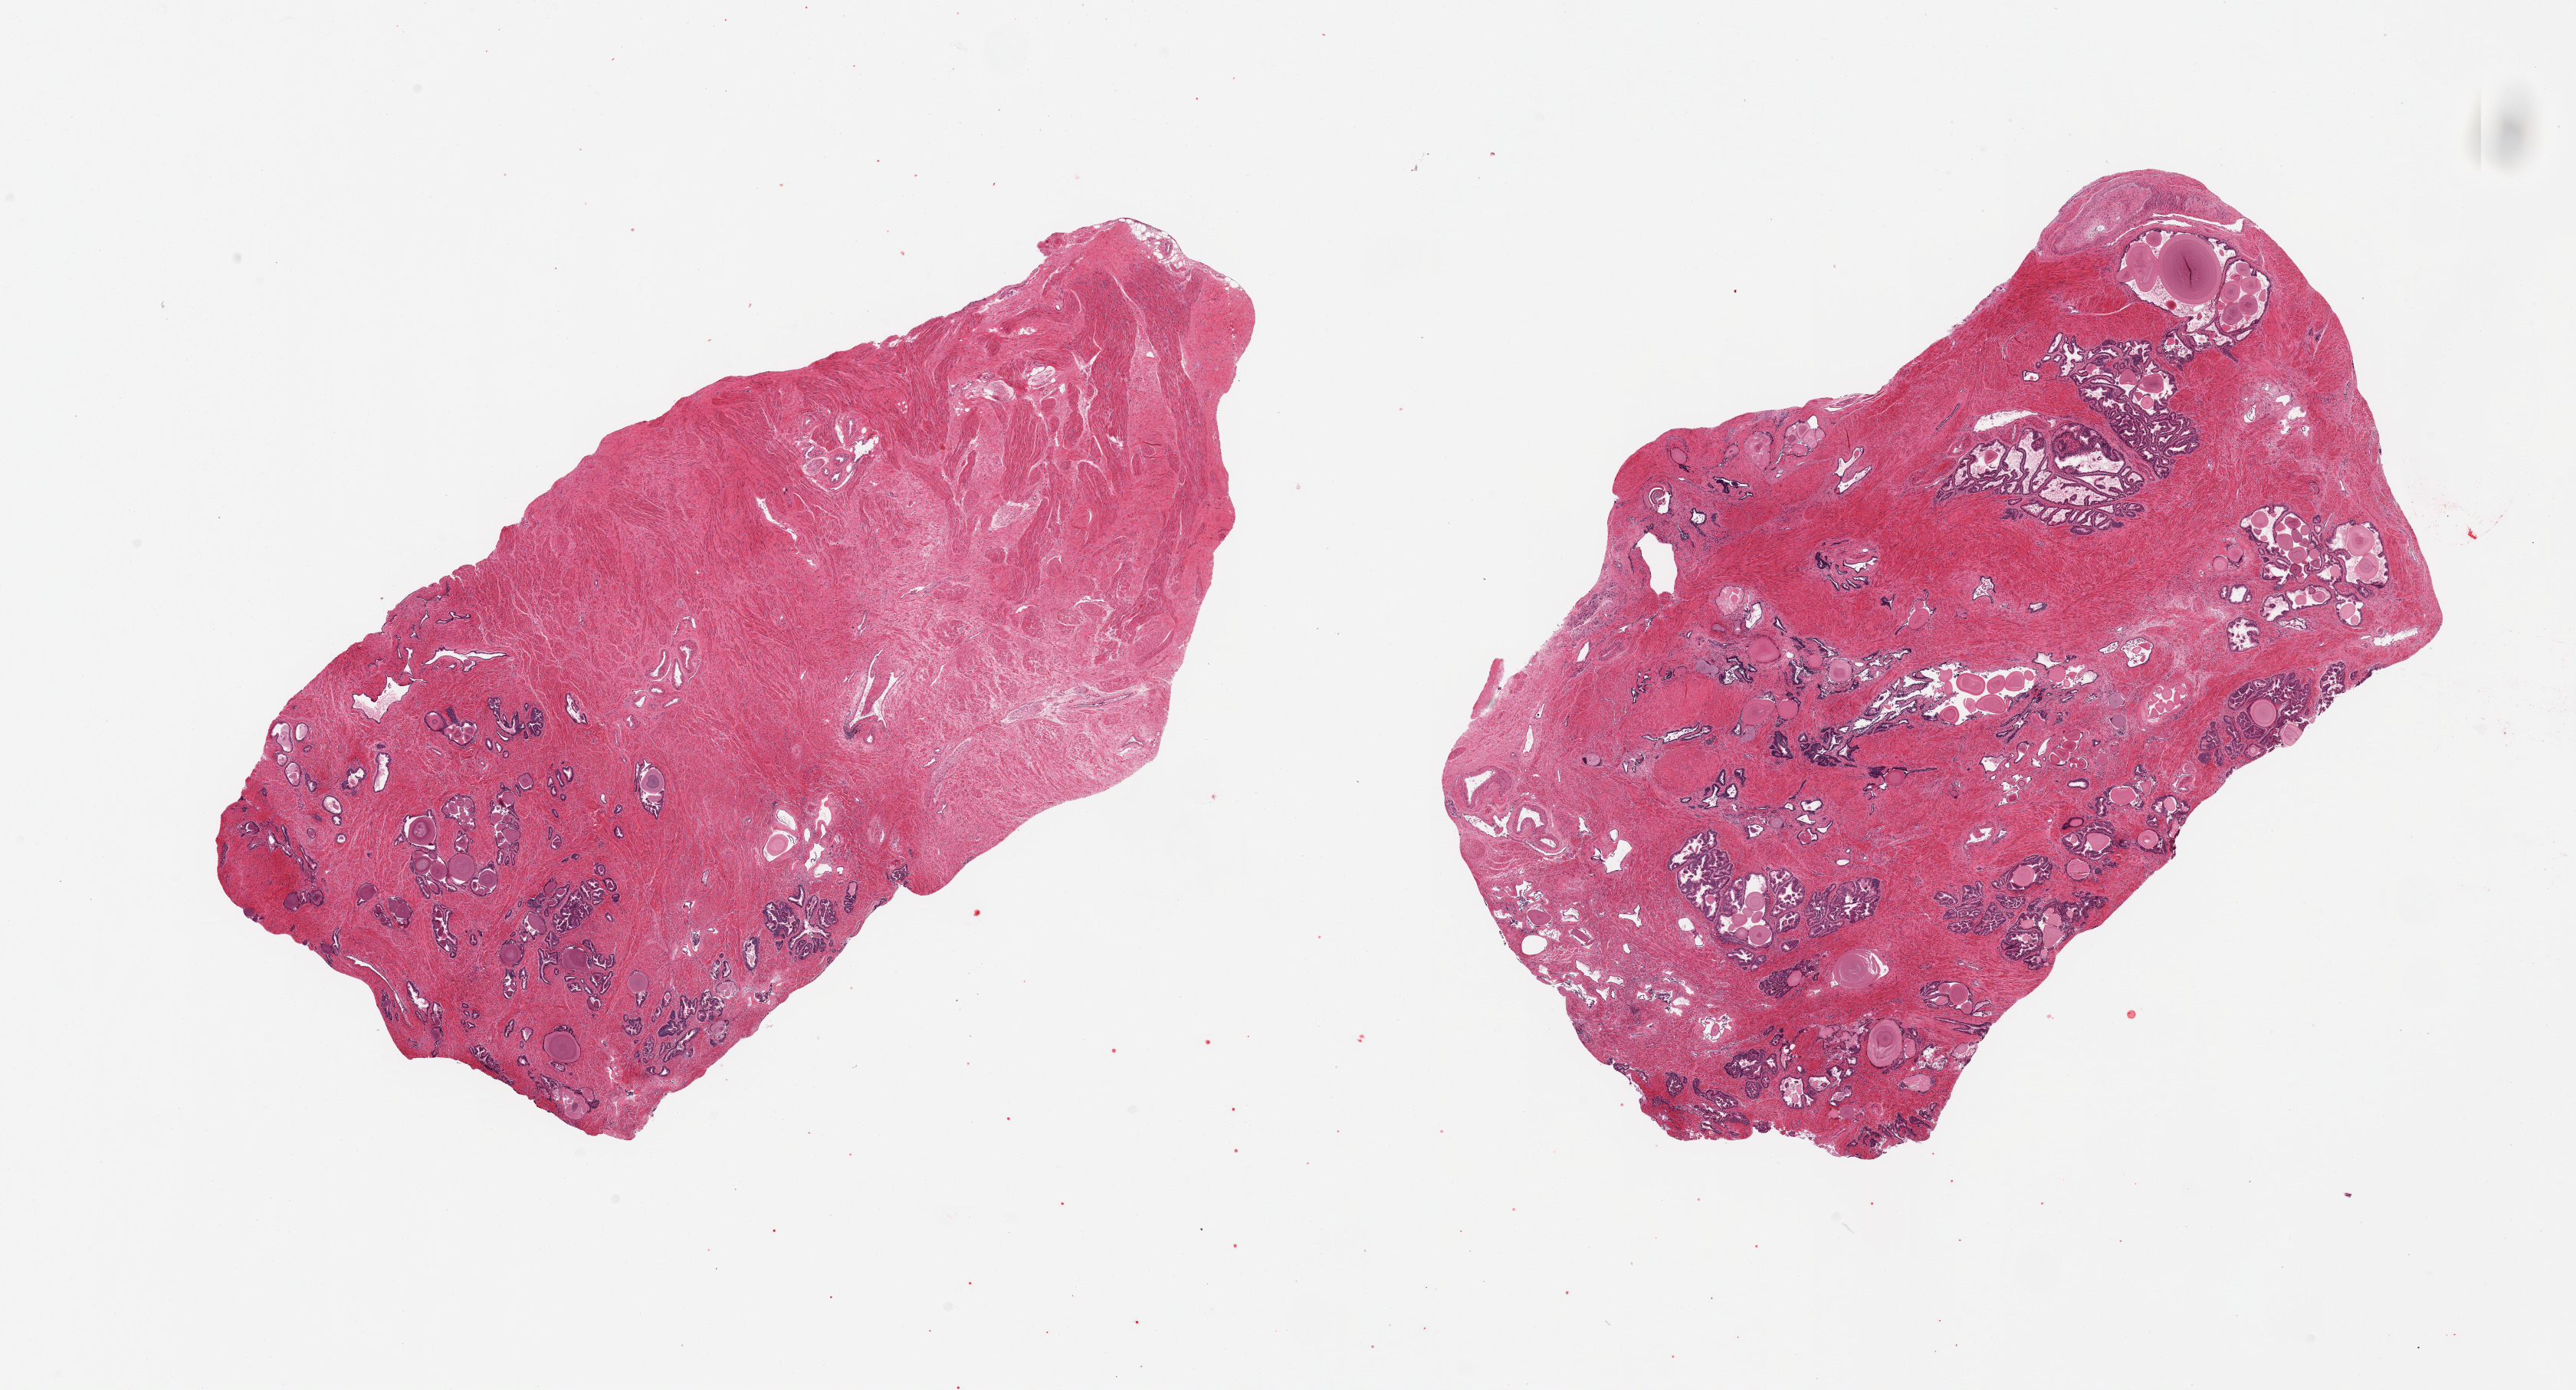
Digitized hematoxylin and eosin (H&E)-stained section, brightfield, shown as a low-resolution overview of the whole scanned area (about 26.6 x 14.3 mm), PAXgene-fixed, paraffin-embedded tissue, target tissue: prostate, tissue donor sample. Donor sex: male.
Pathologist's review note for this sample: 2 pieces, hyperplastic glandular pattern, fairly well preserved.